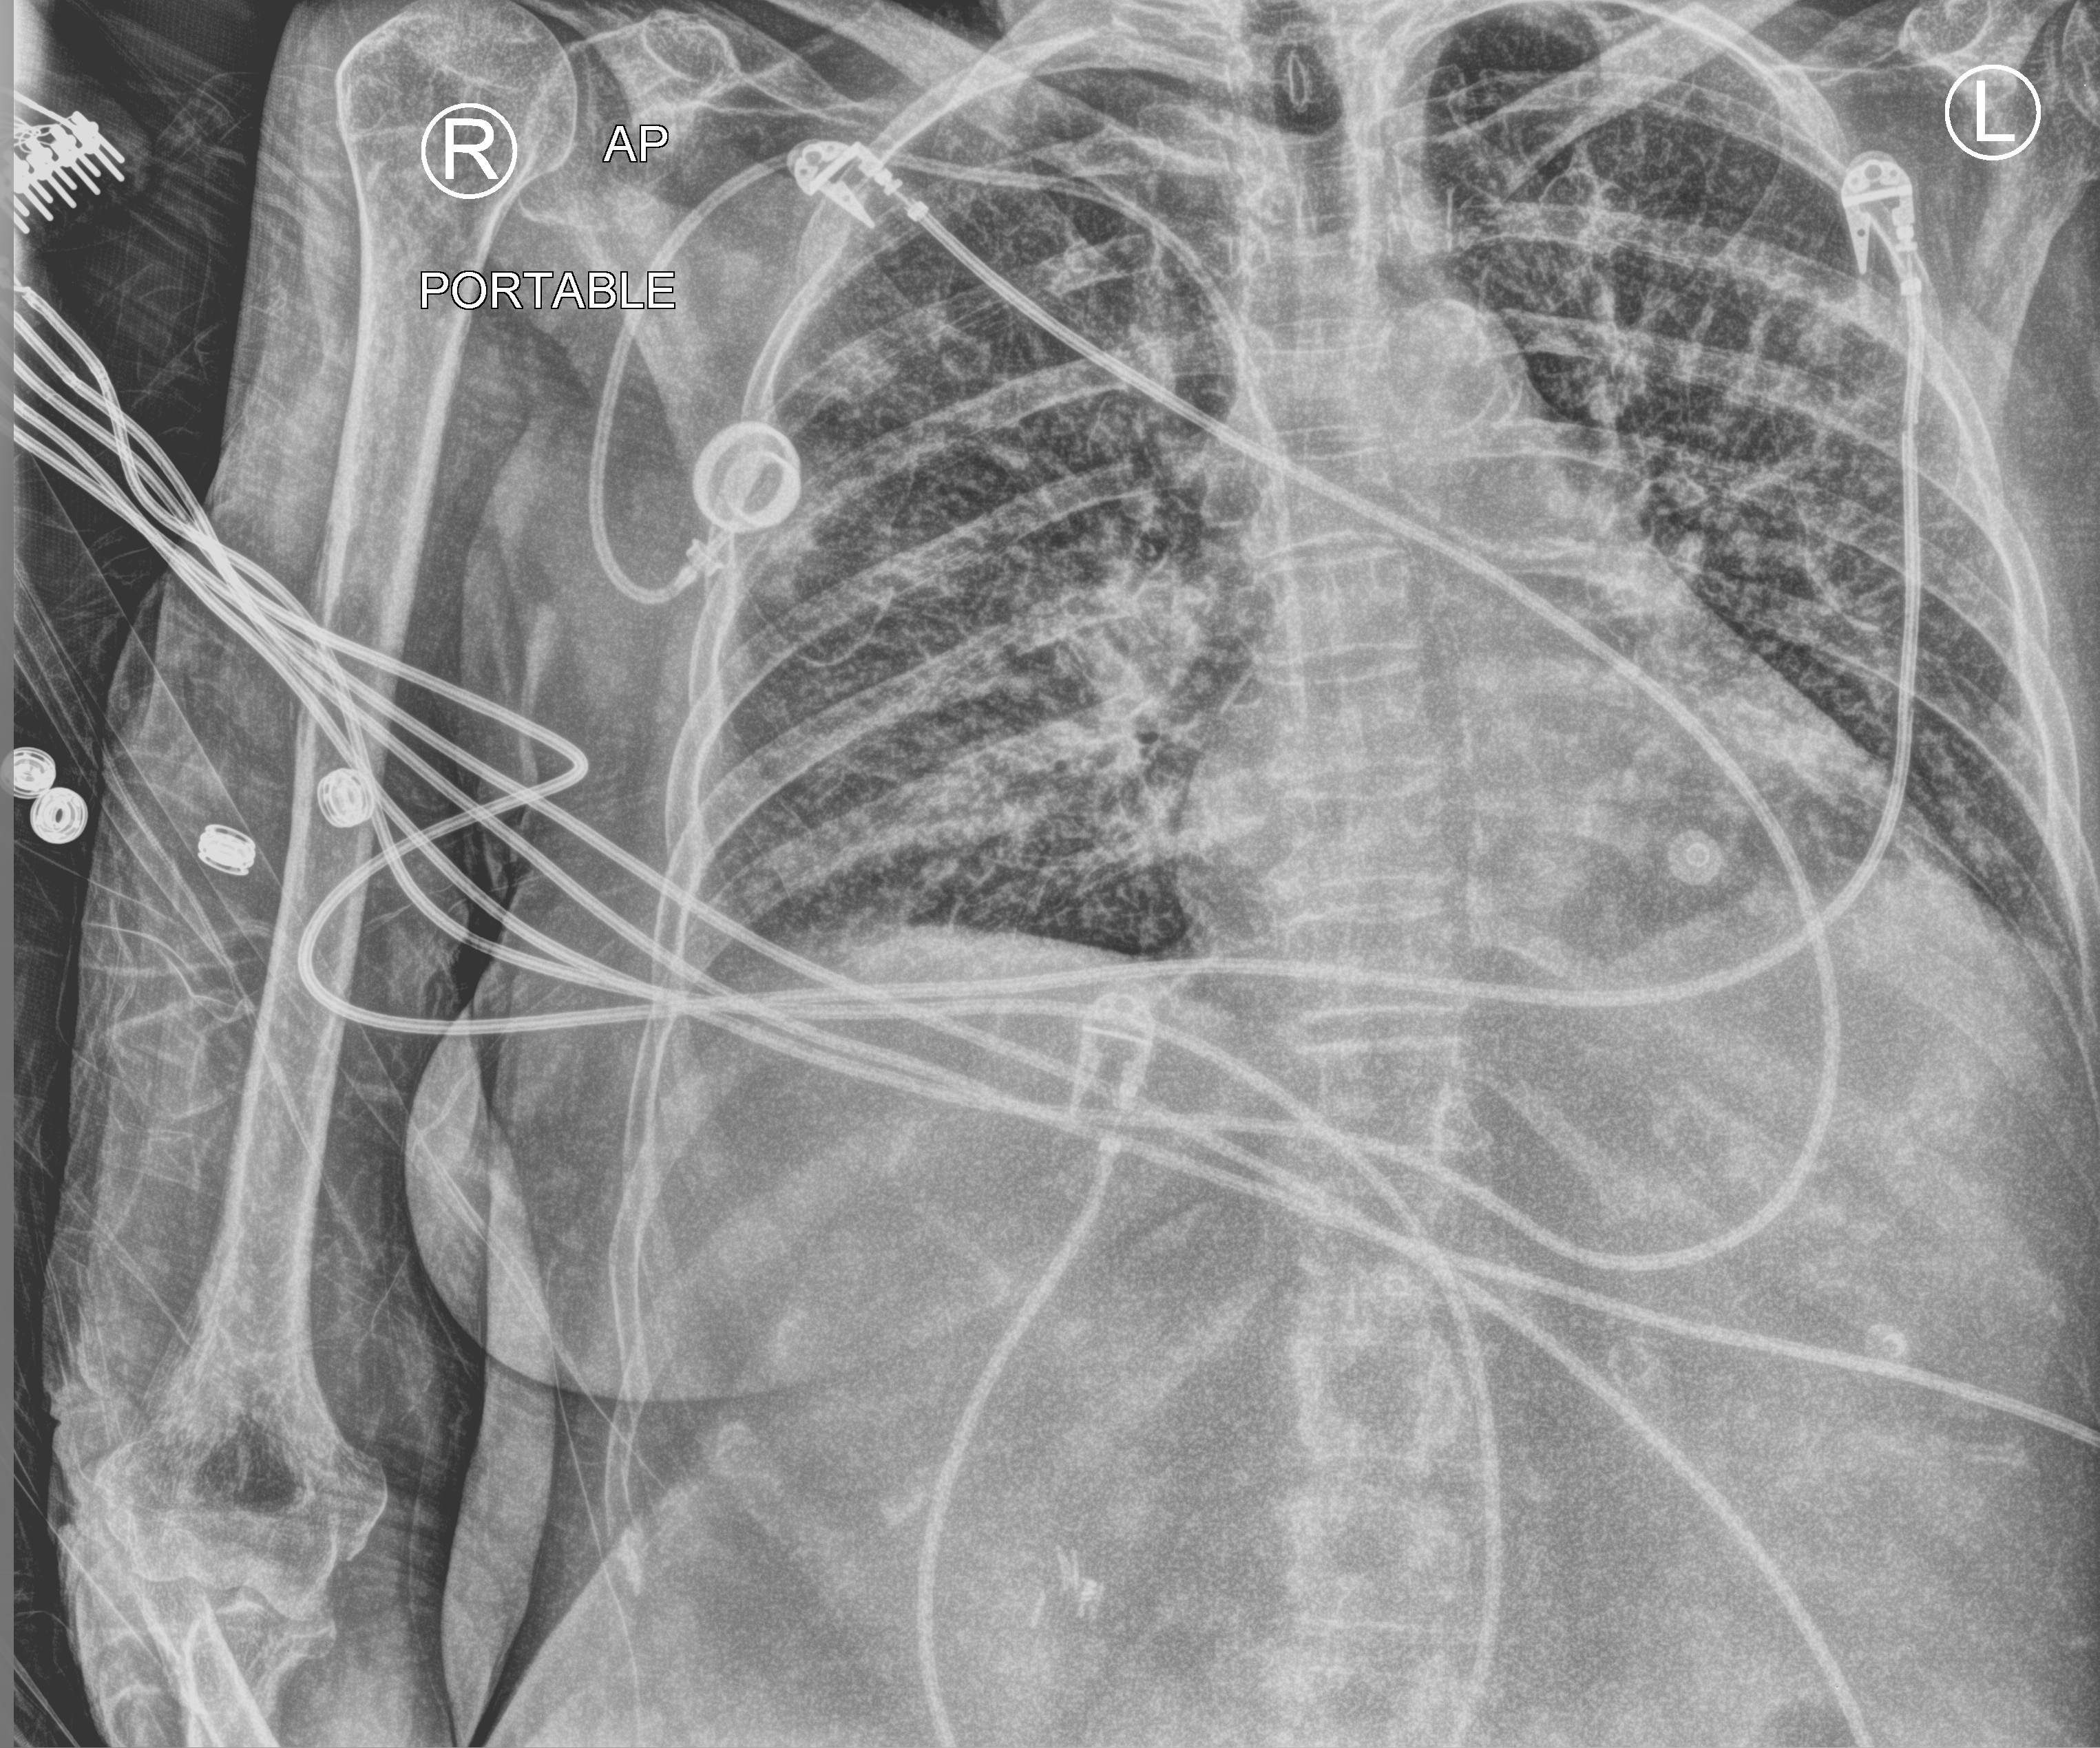
Portable chest radiograph; anteroposterior (AP) projection. Patient hospitalised with COVID-19; female, aged 75–90 years.
From the hospital-stay record, not from the radiograph (when in the stay this image was taken is not recorded): length of hospital stay: 7 days.